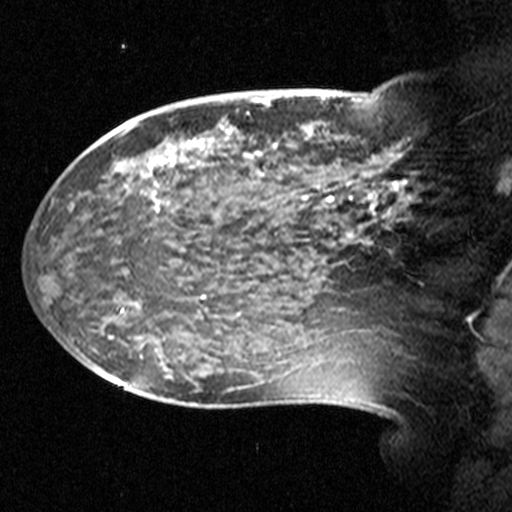
Breast MRI (dynamic contrast-enhanced), one sagittal slice; slice 15 of 44 in the series (ordered by position); dynamic contrast-enhanced study with each time point stored as its own series, time point 2 of 3 at this slice position (early post-contrast, ordered by acquisition time); 1.5 T; TE 4.5 ms, TR 11 ms; 3 mm slice thickness; 512 × 512 image matrix, field of view 240 × 240 mm. Patient: female, 38 years. Case-level facts recorded for this patient, not image findings: setting: breast cancer imaged before/during neoadjuvant chemotherapy; receptor status: HR-positive, HER2-negative.
Structures marked on this image (semi-automatically segmented with operator editing):
- analysis volume of interest (the breast-tissue region the enhancement analysis was run in; not a lesion): box from (x=124, y=106) to (x=405, y=245) px
- tumour enhancement mask (voxels above the 90 % enhancement threshold inside the analysis volume of interest): (x=188, y=142)–(x=405, y=187)